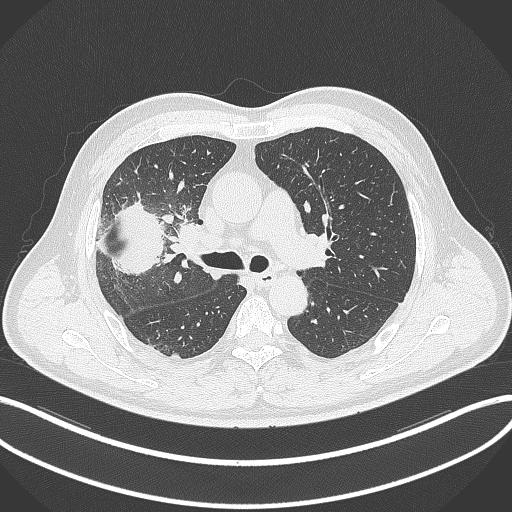
Chest CT, one axial slice. Position 208 of 348 along the scan axis. Lung window (W 1500 / L -600 HU). 1 mm slice thickness. 512 × 512 image matrix. Male patient, age 55 years. Case-level facts recorded for this patient, not image findings: clinical TNM (as recorded): T3 N2 M1.
Outlined on this slice (bounding box drawn by a radiologist):
- lung tumour (recorded histology: adenocarcinoma): bounding box <104,191,171,276> (left, top, right, bottom; pixels)